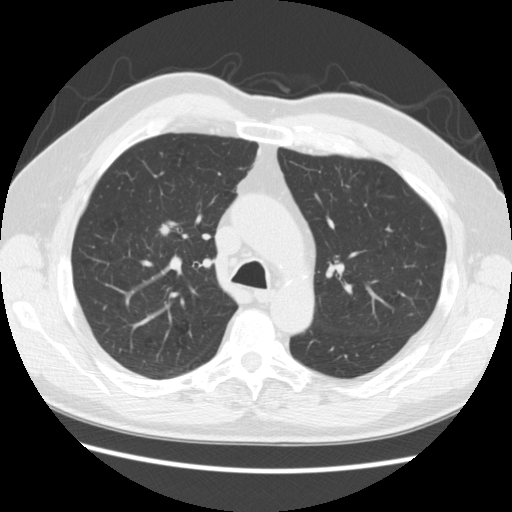
Low-dose screening chest CT, one axial slice. Position 178 of 259 along the scan axis. Reconstruction kernel STANDARD. Lung window (W 1500 / L -600 HU). 2.5 mm slice thickness. 512 × 512 image matrix, field of view 360 × 360 mm.
Structures marked on this image (manually delineated by an expert):
- lesion 1 (tumor, upper lobe of right lung): bounding box <159,224,171,236> (left, top, right, bottom; pixels)